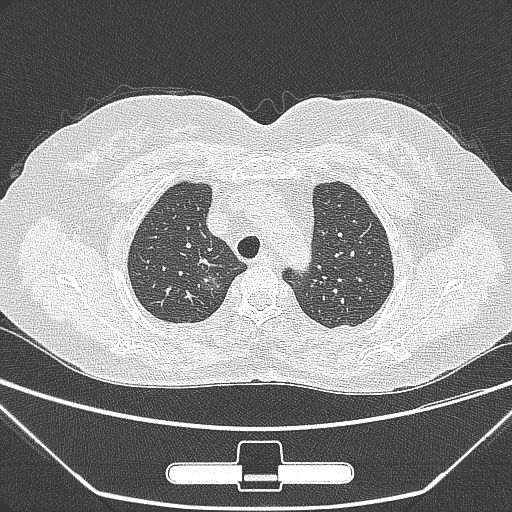
Chest CT, one axial slice. Position 226 of 275 along the scan axis. Lung window (W 1500 / L -600 HU). 512 × 512 image matrix, field of view 356 × 356 mm. Female patient, age 63 years. Case-level facts recorded for this patient, not image findings: clinical TNM (as recorded): T1a N0 M0.
Structures marked on this image (rectangle marked by the reading radiologist):
- lung tumour (recorded histology: adenocarcinoma): box from (x=189, y=257) to (x=231, y=304) px